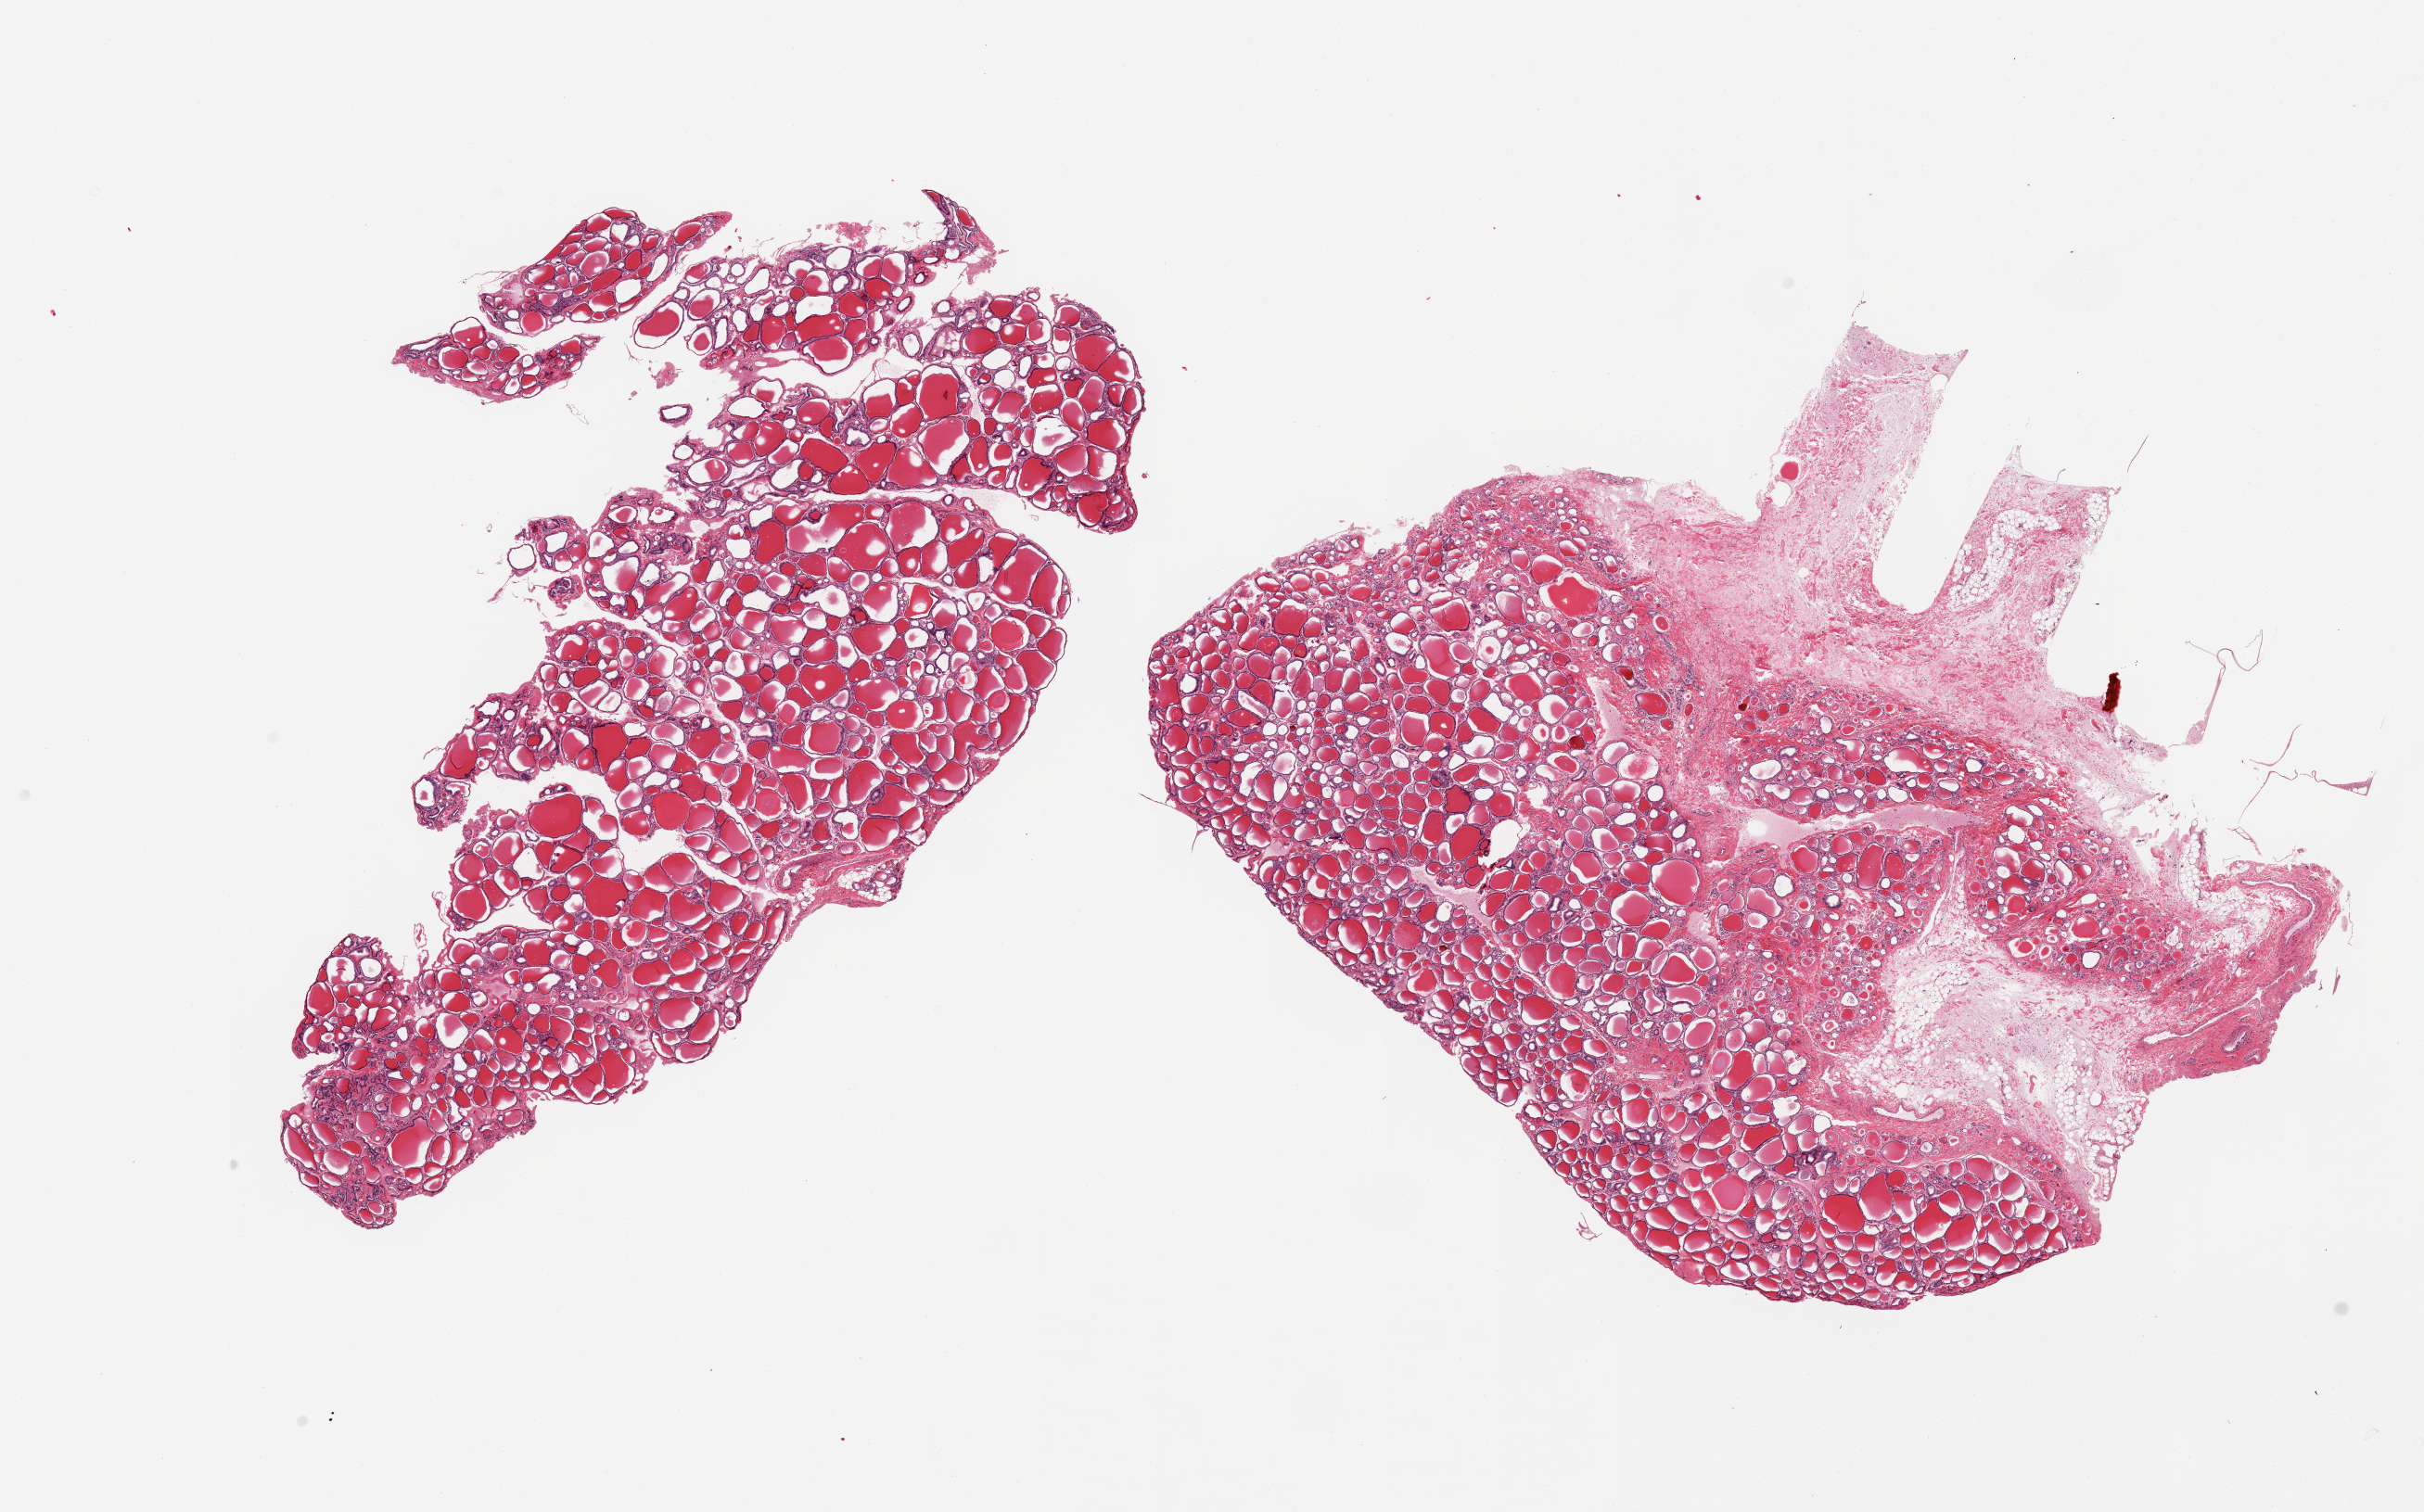
Digitized haematoxylin and eosin-stained section — a low-resolution overview of the entire scanned area, about 20.7 x 12.9 mm (from a 20x scan), PAXgene-fixed, paraffin-embedded tissue, section of thyroid (target tissue), donor tissue sample. Donor sex: male.
Pathologist's review note for this sample: 2 pieces; one includes ~30% mildly autolyzed fat and connective tissue.